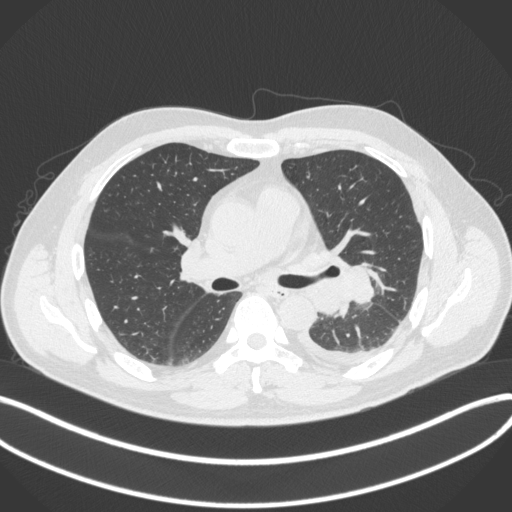
Chest CT, one axial slice; position 211 of 350 along the scan axis; reconstruction kernel B31f; 120 kVp; lung window (W 1500 / L -600 HU); 1 mm slice thickness; 512 × 512 image matrix, field of view 400 × 400 mm. Patient: male, 58 years. From the clinical record (not read from this slice): clinical TNM (as recorded): T3 N1 M1b; histopathological grade: G3.
Outlined on this slice (rectangle marked by the reading radiologist):
- lung tumour (recorded histology: small cell carcinoma): box from (x=315, y=258) to (x=376, y=315) px